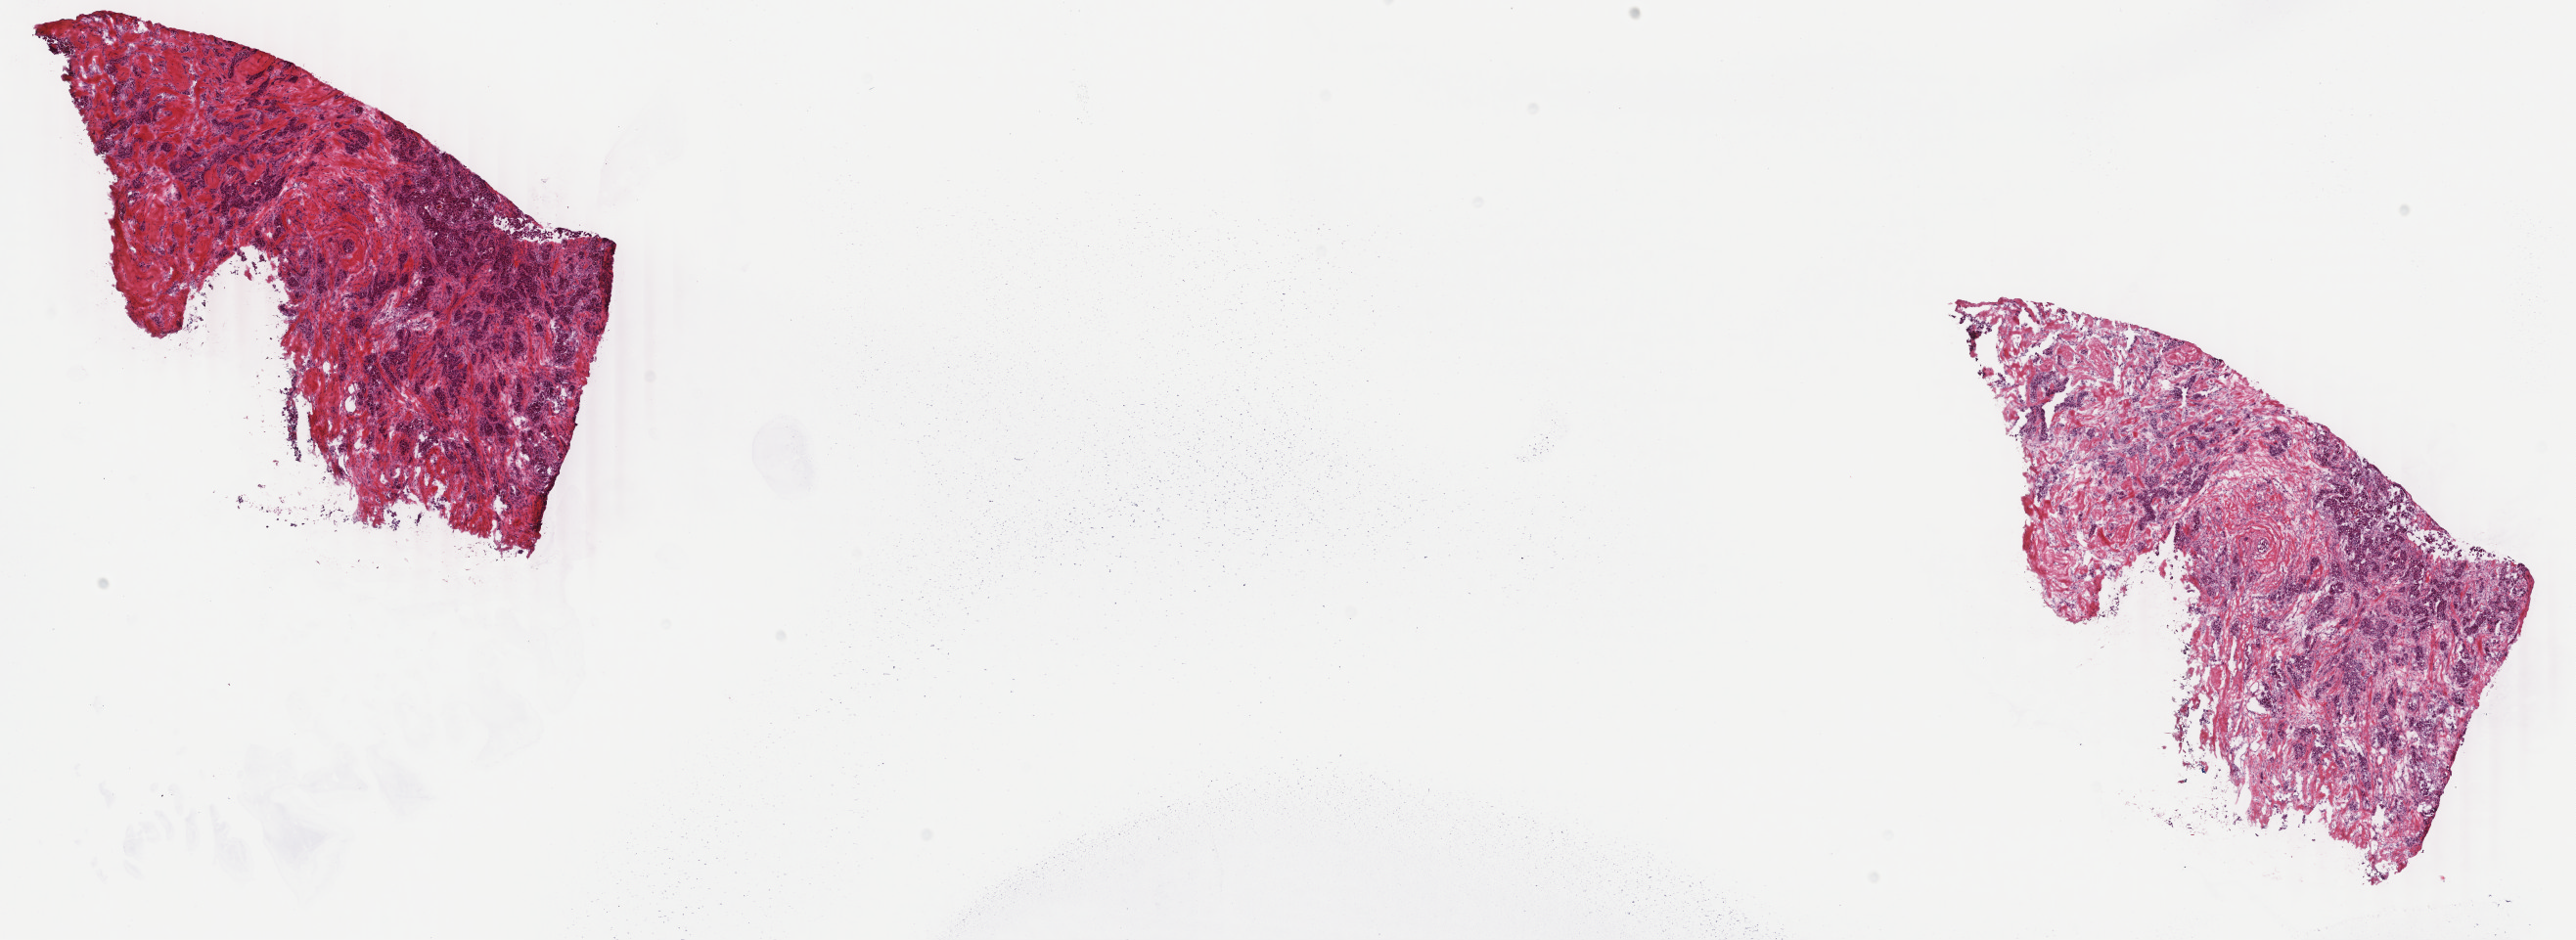
Whole-slide histology image, H&E-stained — shown as a low-resolution overview of the whole scanned area (about 20.9 x 7.6 mm); frozen section; breast, primary tumour sample. Patient: female, age at initial diagnosis 70 years. Pathologist review of this section (percent, as recorded): tumour cells 27%, tumour nuclei 70%, normal cells 2%, stromal cells 70%, necrosis 1%. Infiltration values recorded for this section: lymphocyte infiltration 2%, monocyte infiltration 1%, neutrophil infiltration 0%.
- AJCC pathologic stage: IIIA (7th edition)
- pathologic diagnosis: Infiltrating duct carcinoma, NOS
- TNM: T2 N2a MX
- laterality: right
- lymph nodes positive (case pathology): 5 of 17 examined